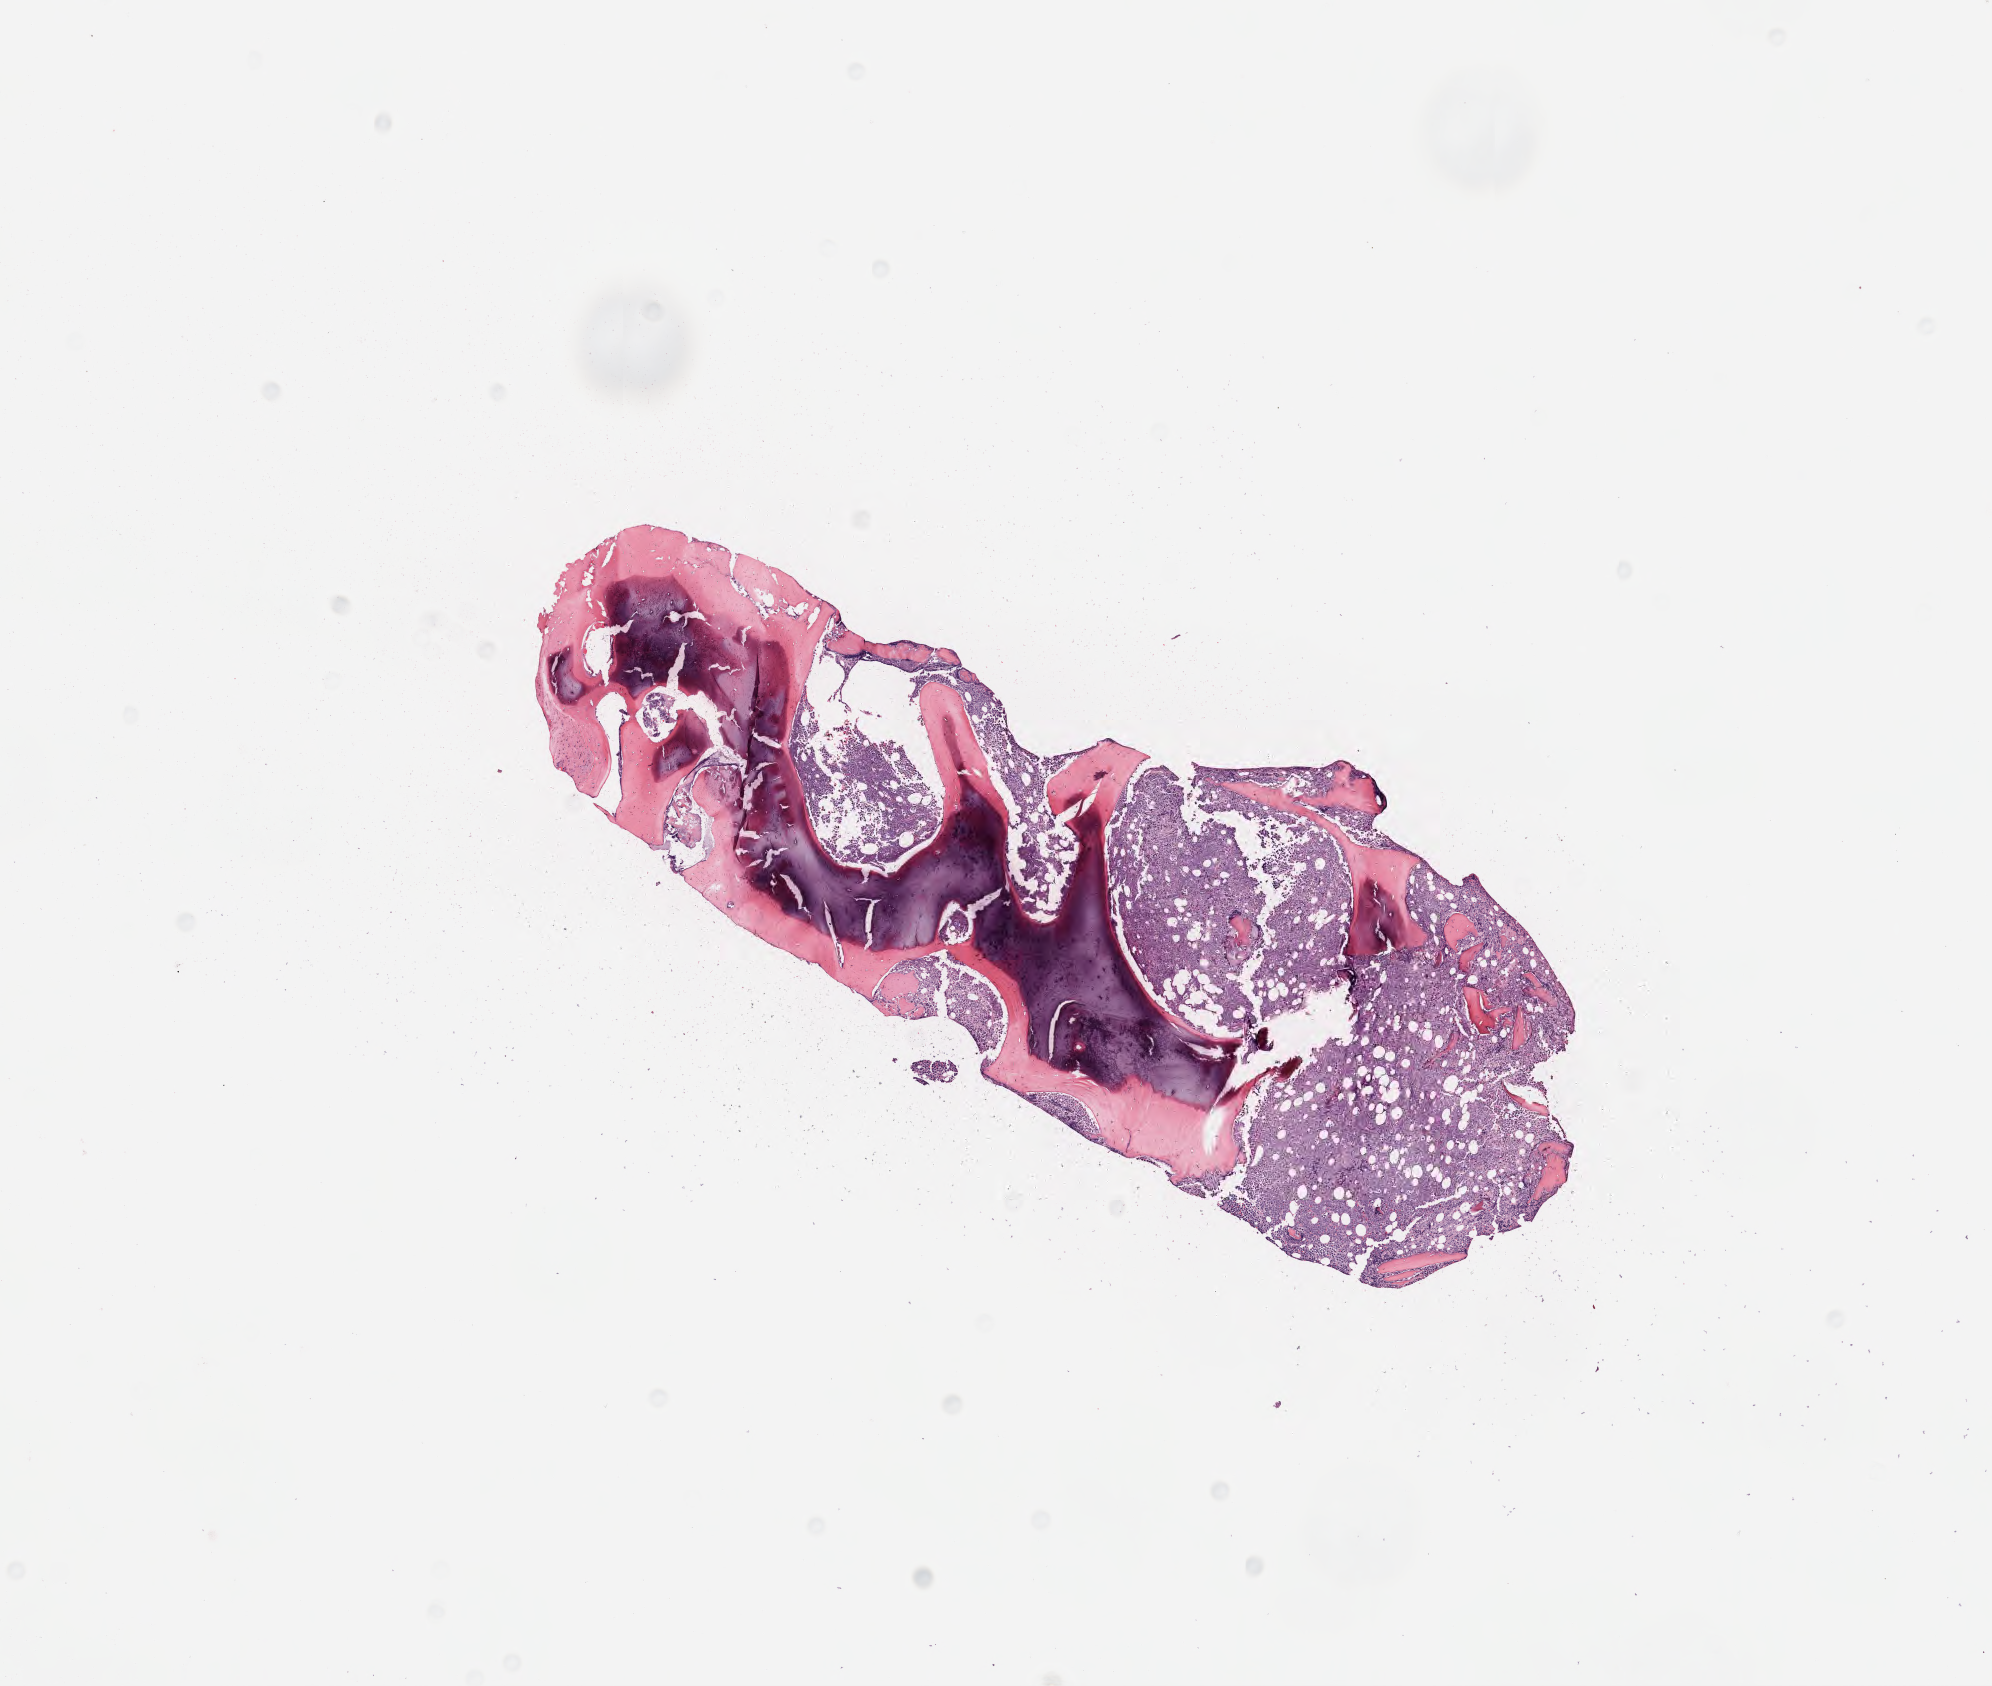
Digitized haematoxylin and eosin-stained section — low-resolution overview of the scanned area, about 8.0 x 6.8 mm, specimen: tumor tissue, site: bone marrow. Patient male; age 15 years.
Histologic diagnosis: Burkitt lymphoma, NOS.